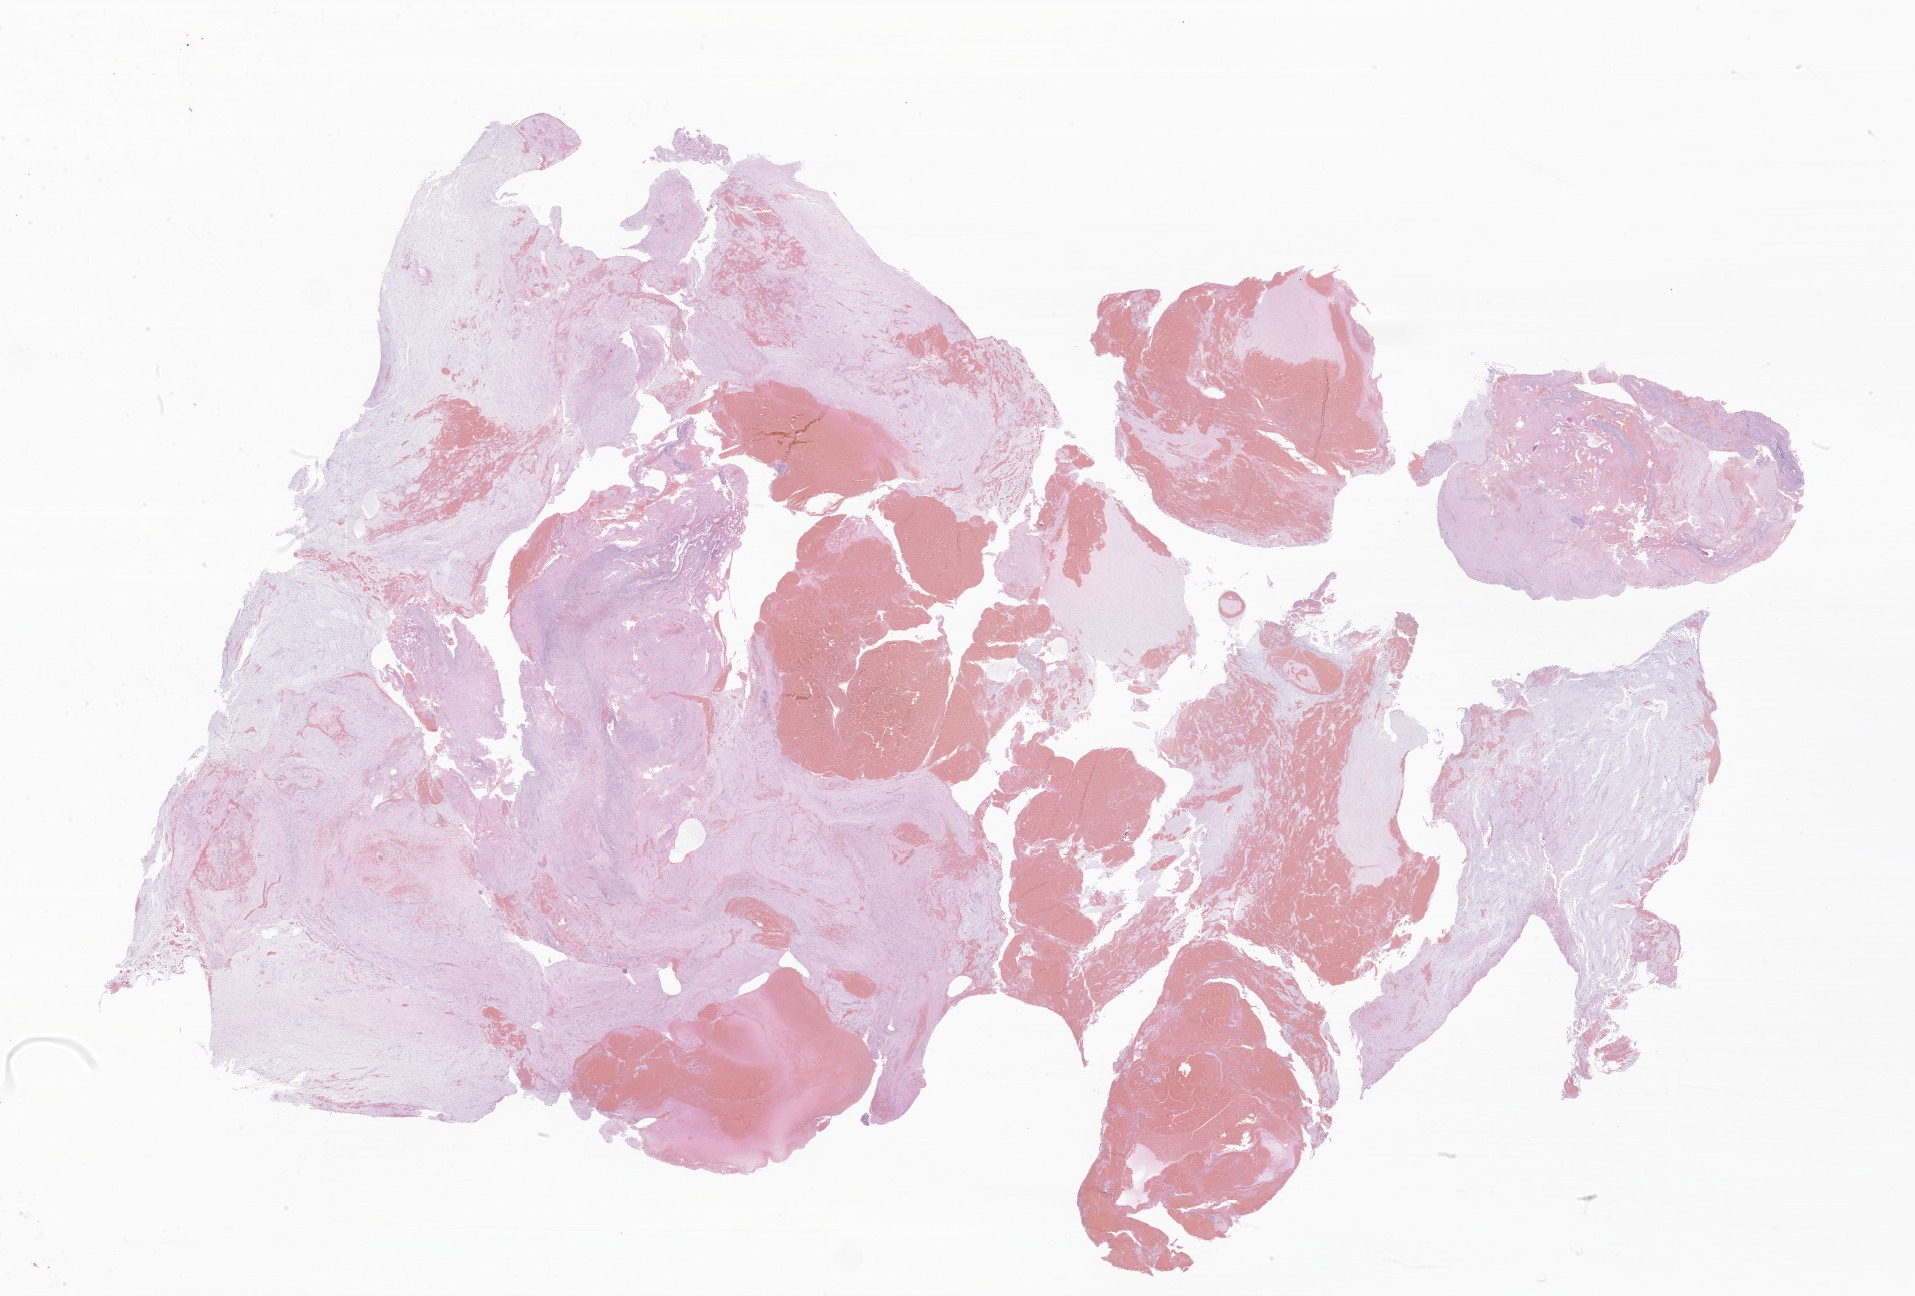
Whole-slide image, hematoxylin and eosin (H&E) stain of tumor tissue from the brain, low-resolution overview of the scanned area, about 32.3 x 21.9 mm, FFPE section. Patient: female, age 88 months (7 years 4 months).
- diagnosis (ICD-O-3 morphology term): Pilocytic astrocytoma